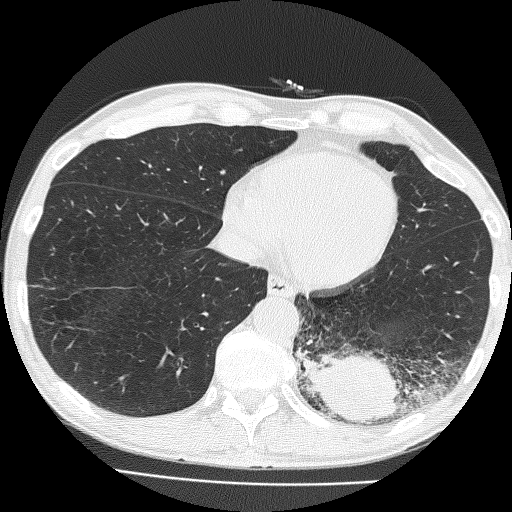
Low-dose screening chest CT, one axial slice. Reconstruction kernel FC51. Lung window (W 1500 / L -600 HU). 2 mm slice thickness. 512 × 512 image matrix, field of view 324 × 324 mm.
Outlined on this slice (manually delineated by an expert):
- lesion 1 (tumor, lower lobe of left lung): bounding box (x1, y1, x2, y2) in pixels: (296, 346, 402, 425)